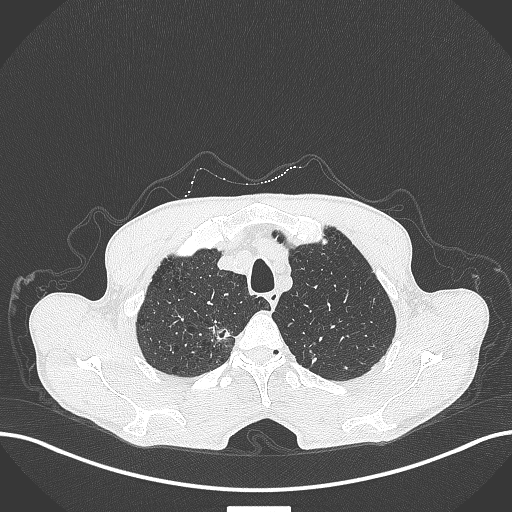
Chest CT, one axial slice. Position 366 of 445 along the scan axis. Reconstruction kernel B70f. 120 kVp. Lung window (W 1500 / L -600 HU). 1 mm slice thickness. 512 × 512 image matrix. Patient: male, 70 years. Case-level facts recorded for this patient, not image findings: clinical TNM (as recorded): T1a N0 M0.
Annotated regions visible in this slice (rectangle marked by the reading radiologist):
- lung tumour (recorded histology: adenocarcinoma): bounding box [x1, y1, x2, y2] px = [208, 321, 236, 342]